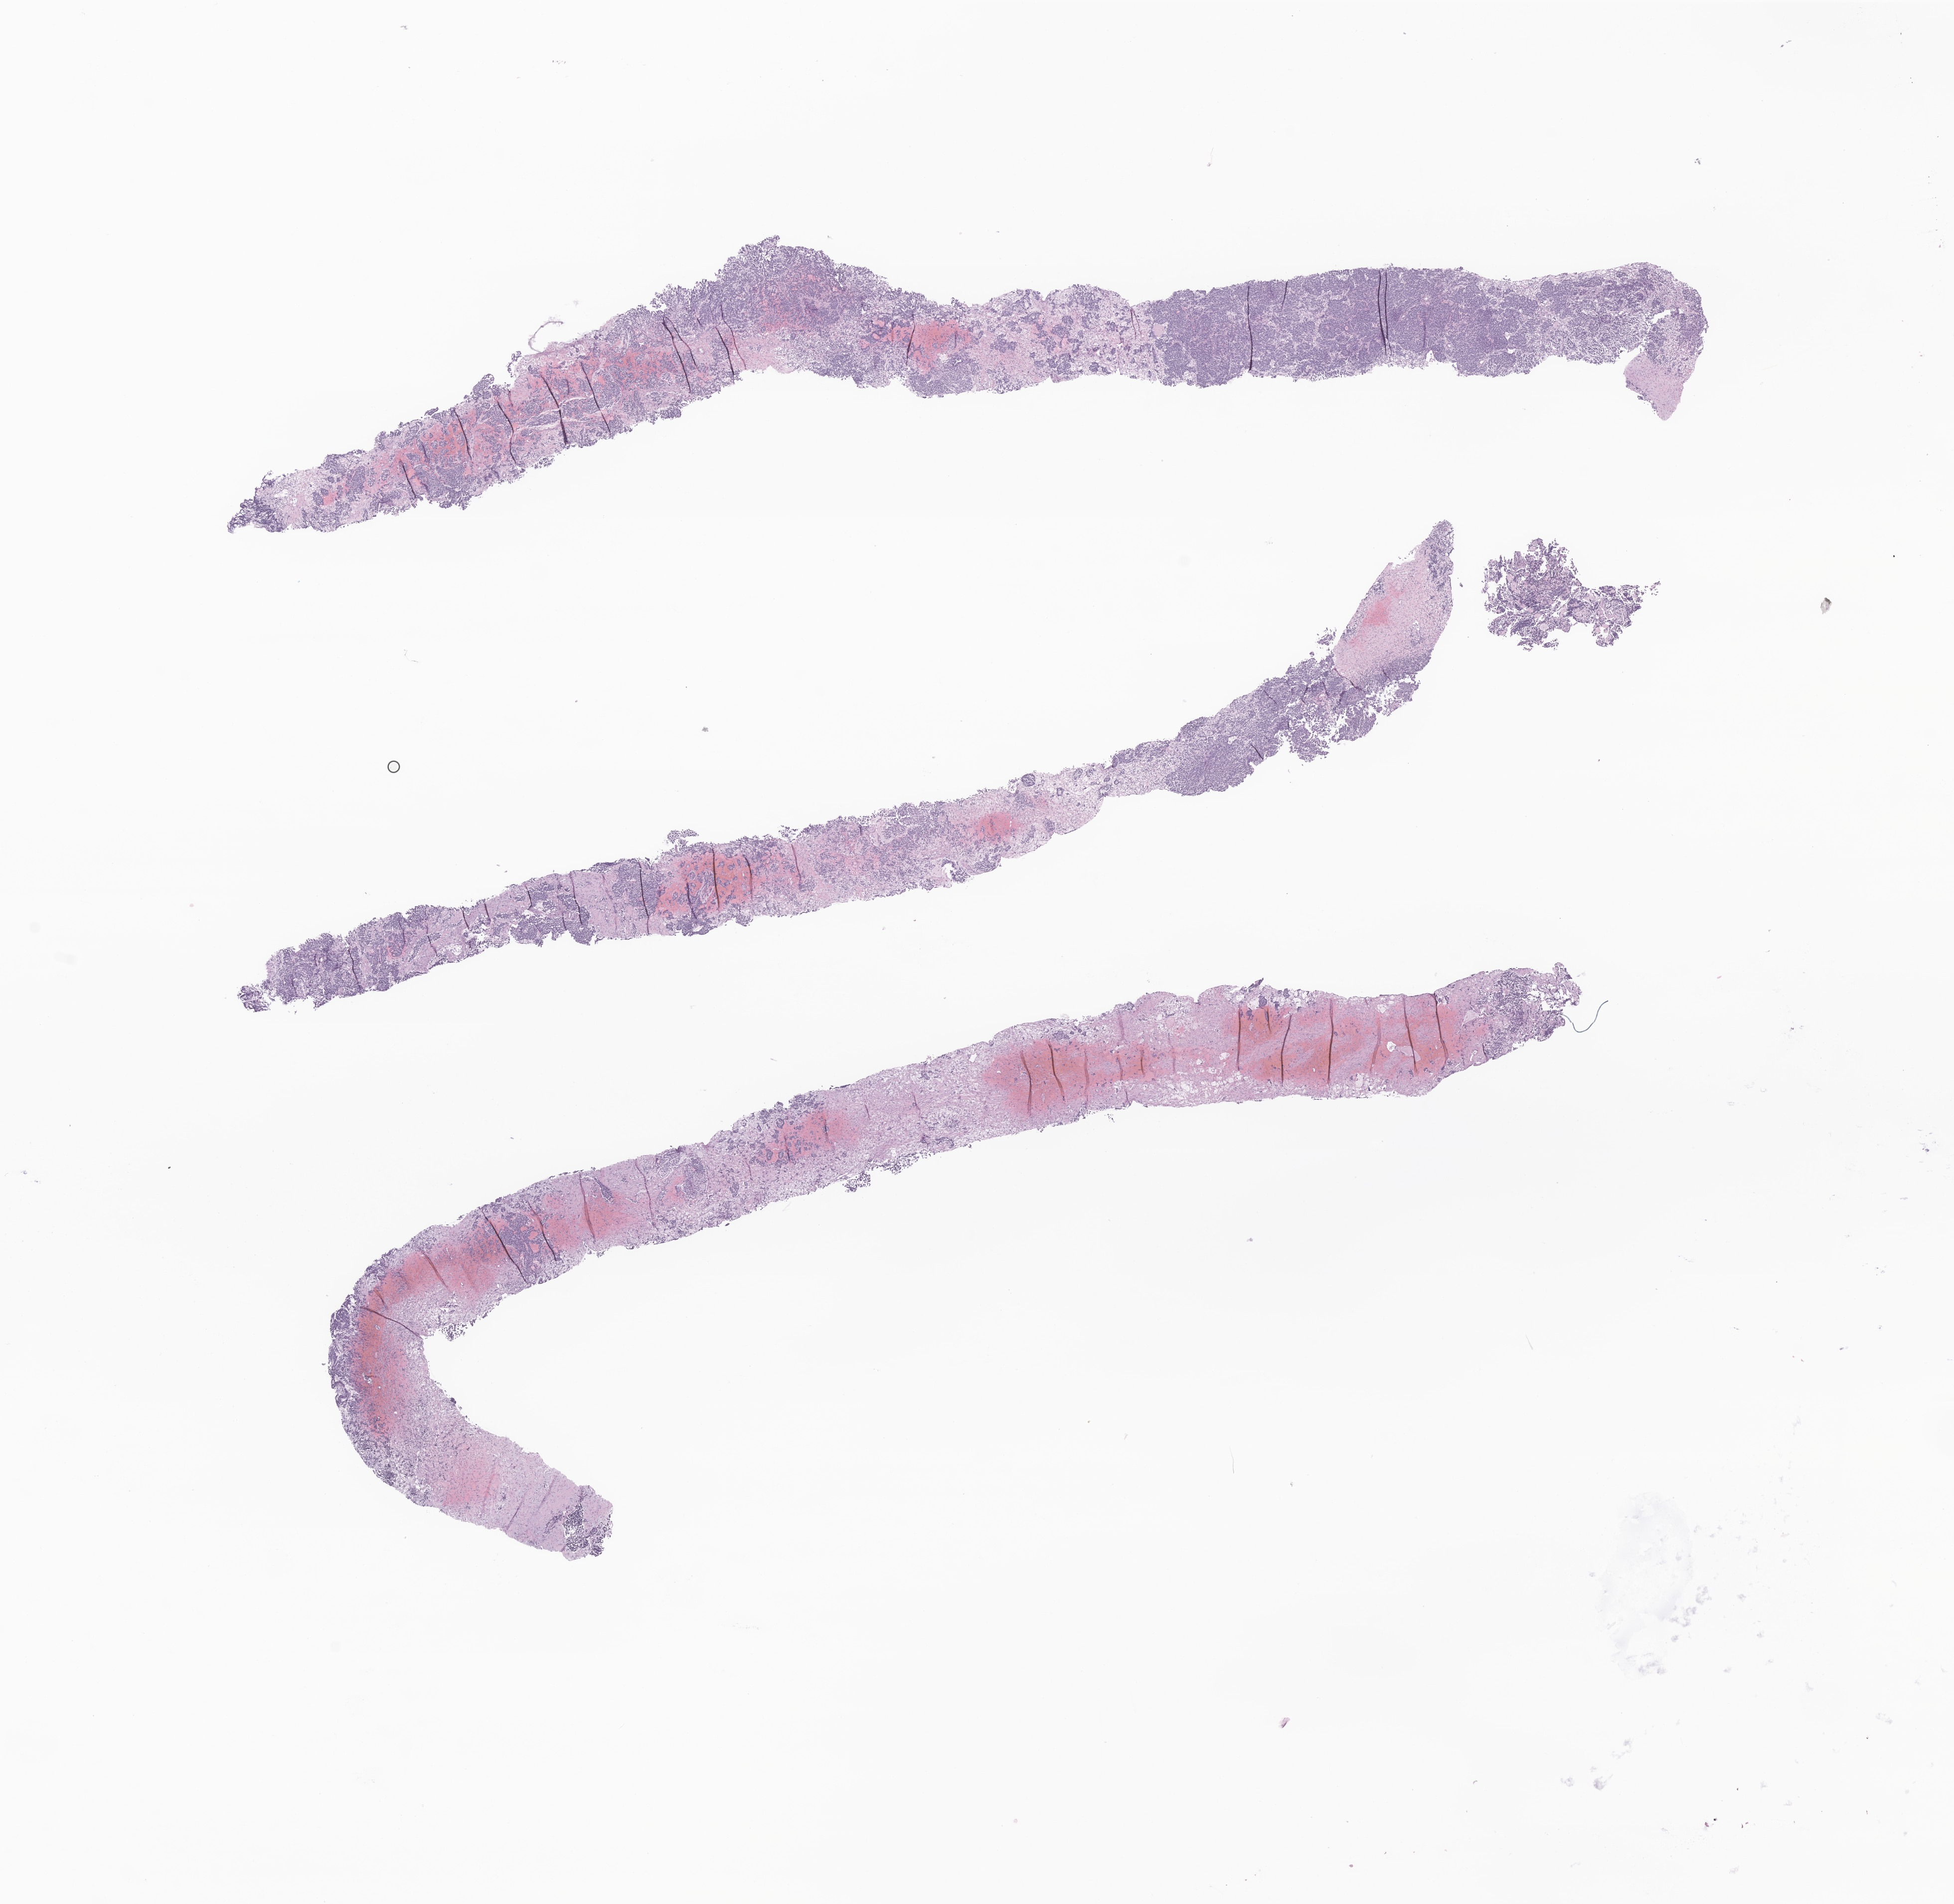
Whole-slide image, H&E stain of tumor tissue from the adrenal gland, whole scanned area (about 16.5 x 16.1 mm) shown as a low-resolution overview, formalin-fixed, paraffin-embedded (FFPE) tissue. Patient: male, age 142 days.
Recorded diagnosis: Neuroblastoma, NOS.